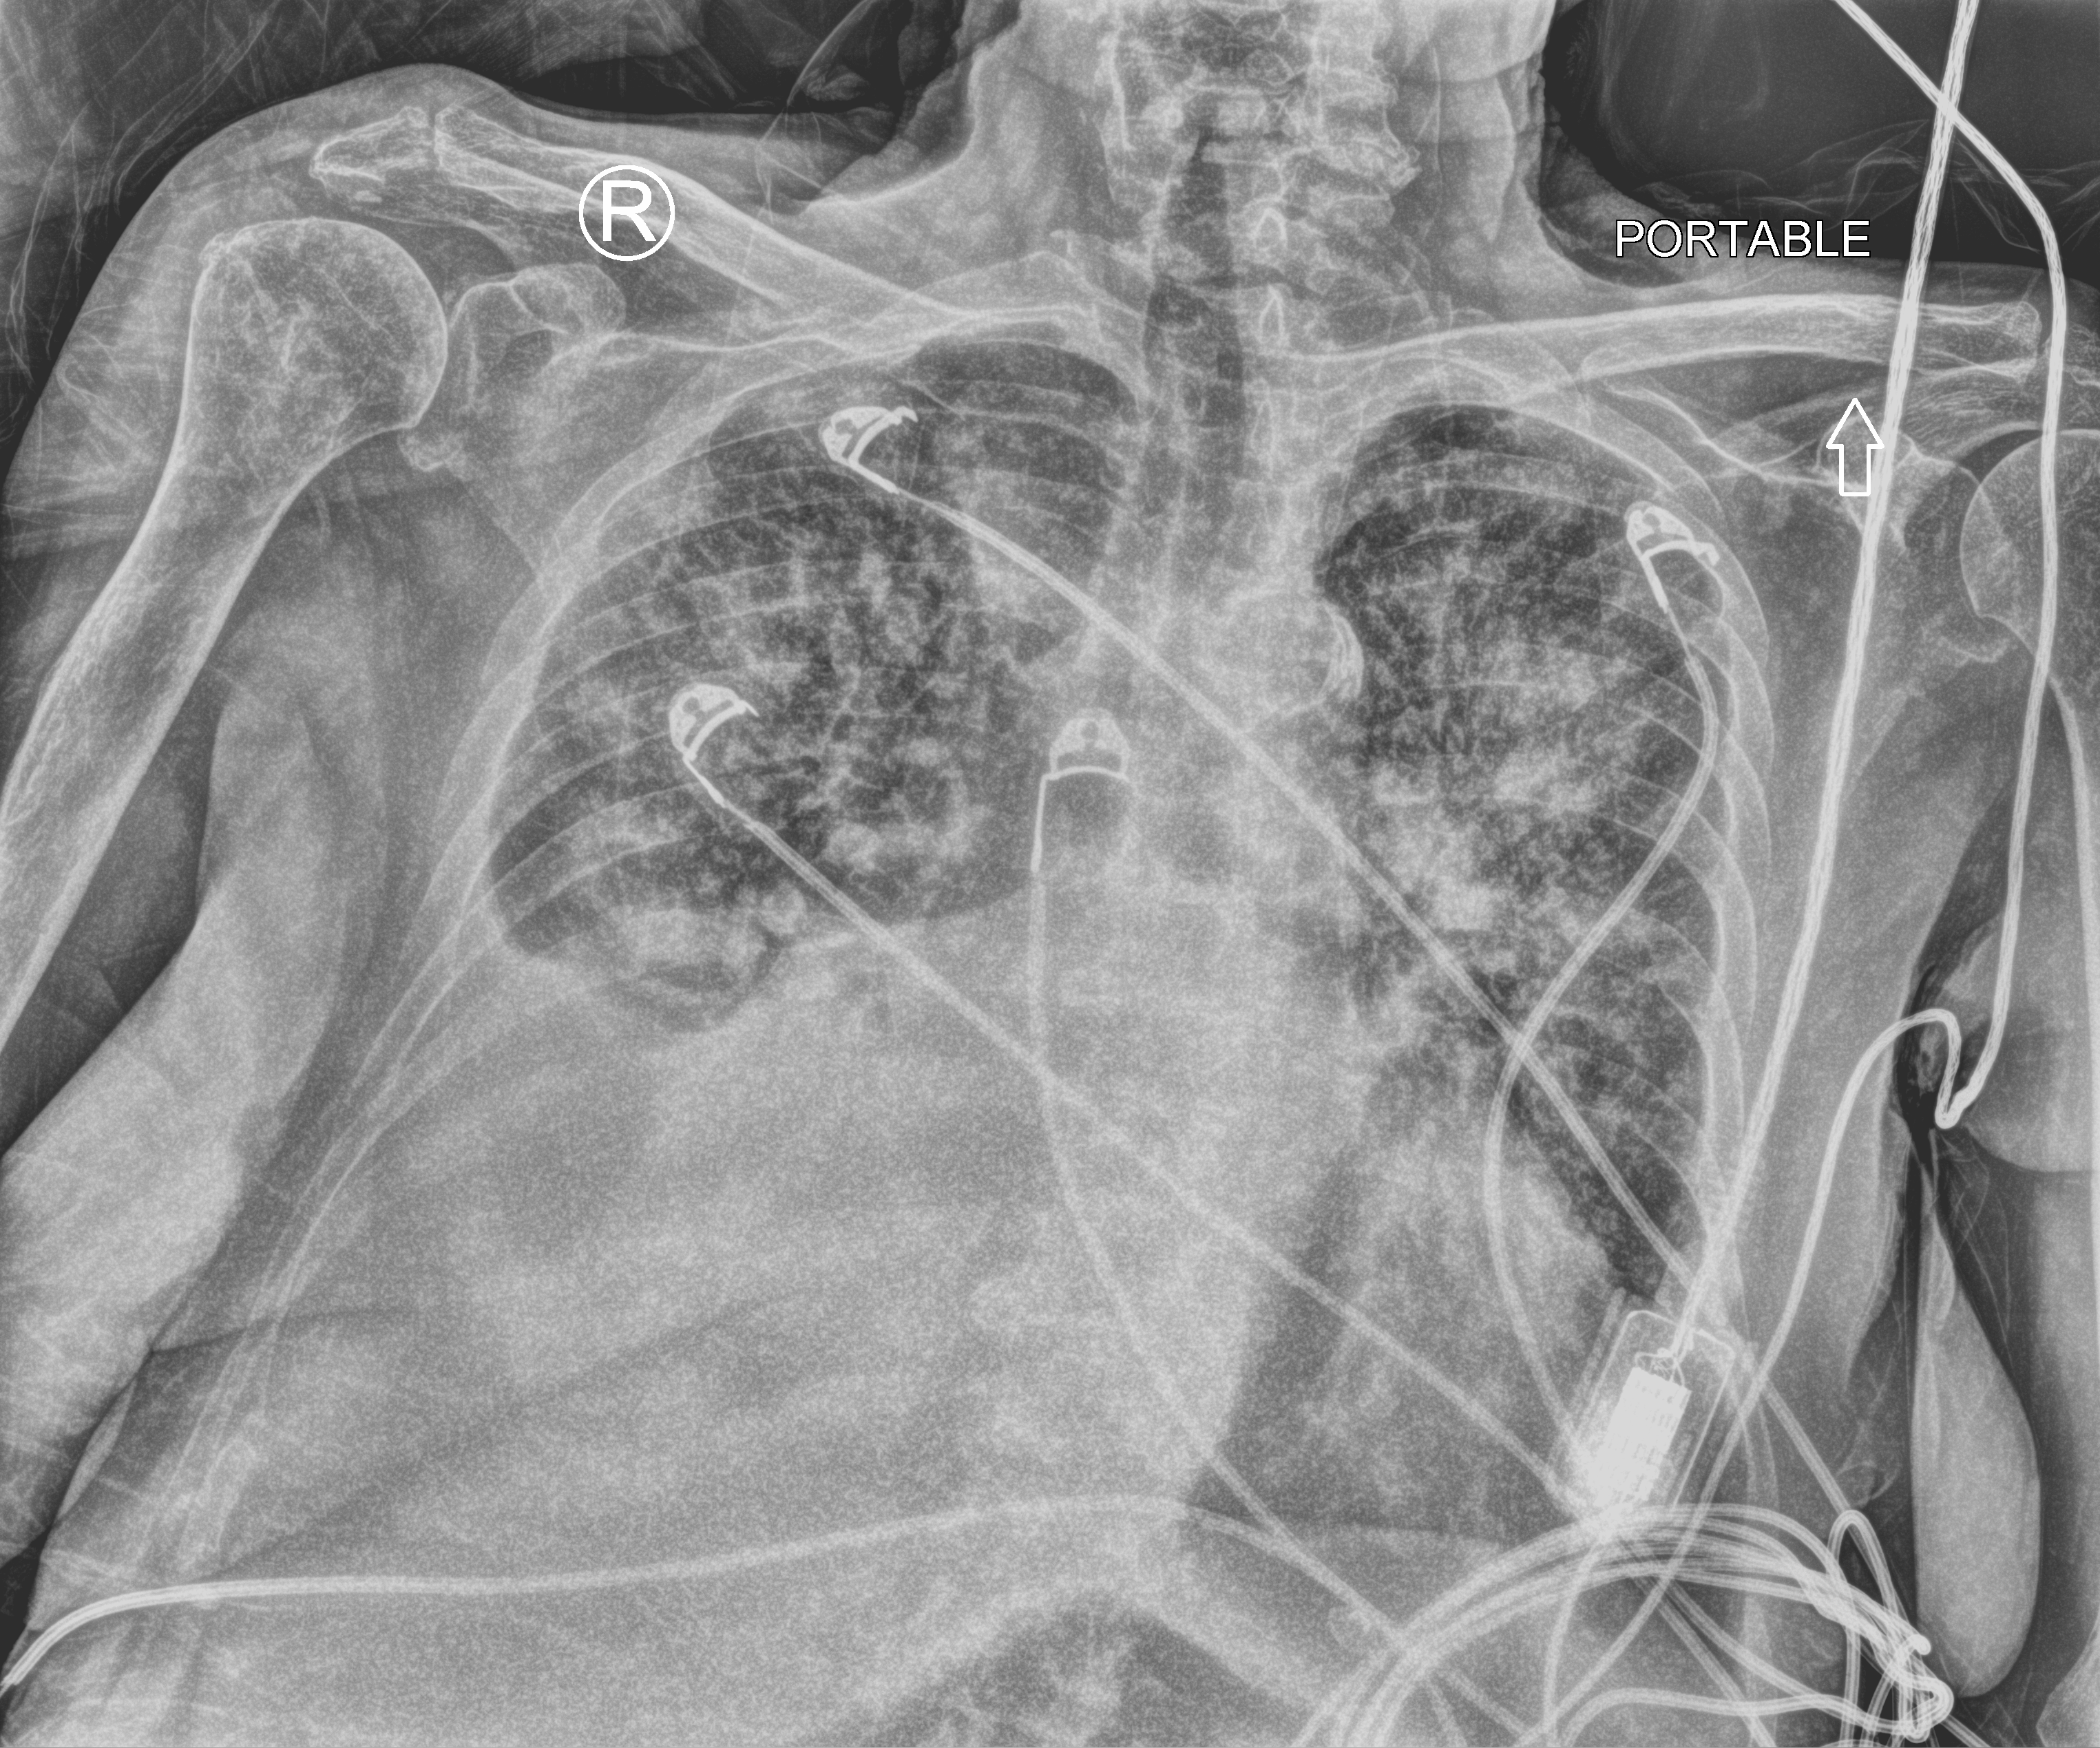
Bedside chest radiograph (computed radiography); anteroposterior (AP) projection. Patient hospitalised with COVID-19; female, aged 75–90 years.
From the hospital-stay record, not from the radiograph (when in the stay this image was taken is not recorded):
- admitted to intensive care during this hospital stay: yes
- length of hospital stay: 2 days